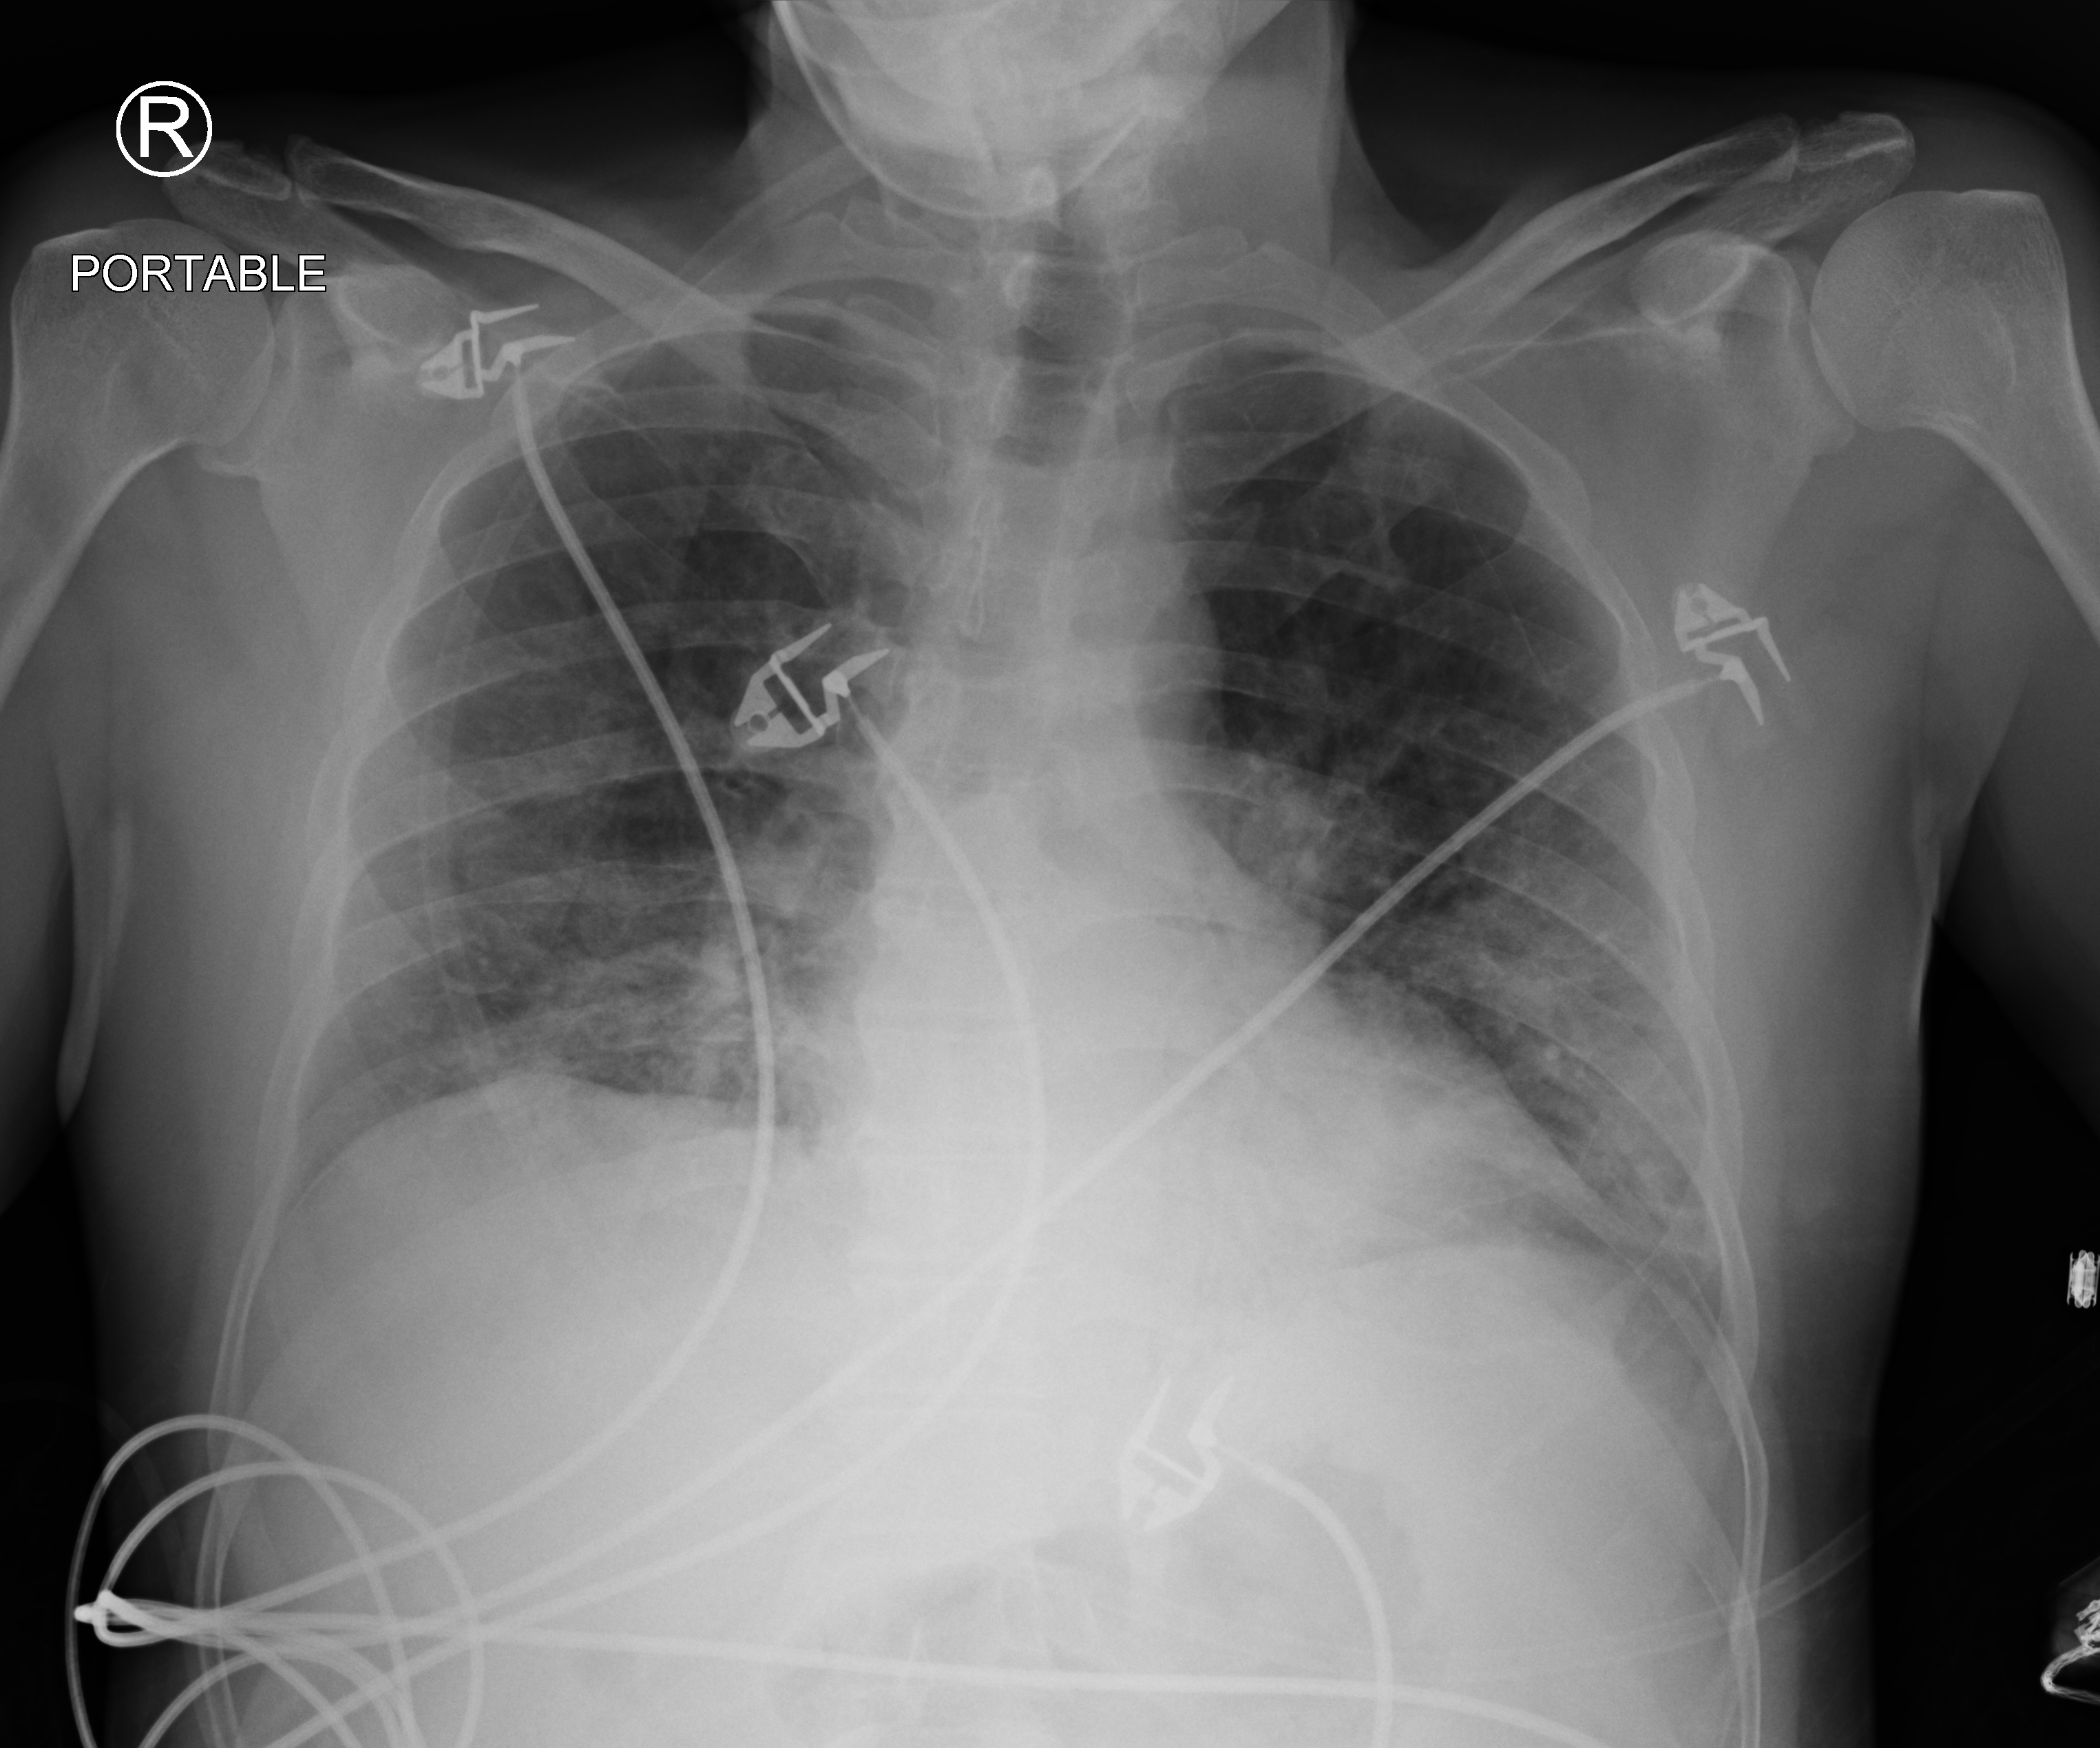
Portable chest radiograph, anteroposterior (AP) projection. Patient hospitalised with COVID-19; male, aged 18–59 years.
Hospital-stay facts (about this admission, not read from this image; timing relative to this image not recorded):
- admitted to intensive care during this hospital stay: no
- other chronic lung disease (admission record): no
- mechanically ventilated during this hospital stay: no